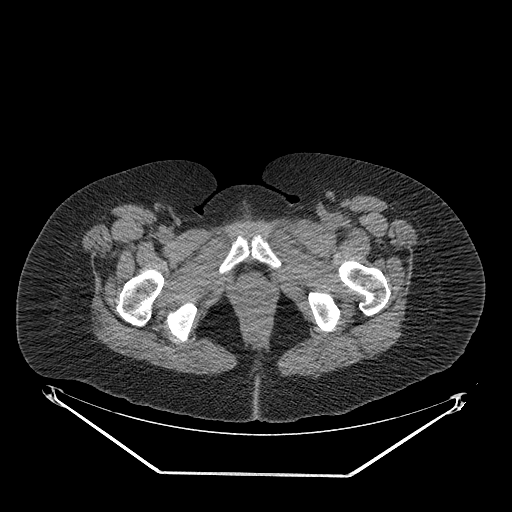
CT of an extremity soft-tissue mass (from a PET/CT study), one axial slice; slice 51 of 267 in the series (ordered by position); reconstruction kernel STANDARD; 140 kVp; soft-tissue window (W 400 / L 40 HU); 3.75 mm slice thickness; 512 × 512 image matrix, field of view 500 × 500 mm. Female patient. From the clinical record (not read from this slice): histological type: myxofibrosarcoma; grade: intermediate; site of the primary tumour: left thigh.
Outlined on this slice (expert contour drawn on MRI and transferred to this co-registered scan by the dataset authors):
- gross tumour volume including surrounding oedema: bounding box (x1, y1, x2, y2) in pixels: (269, 212, 357, 250)